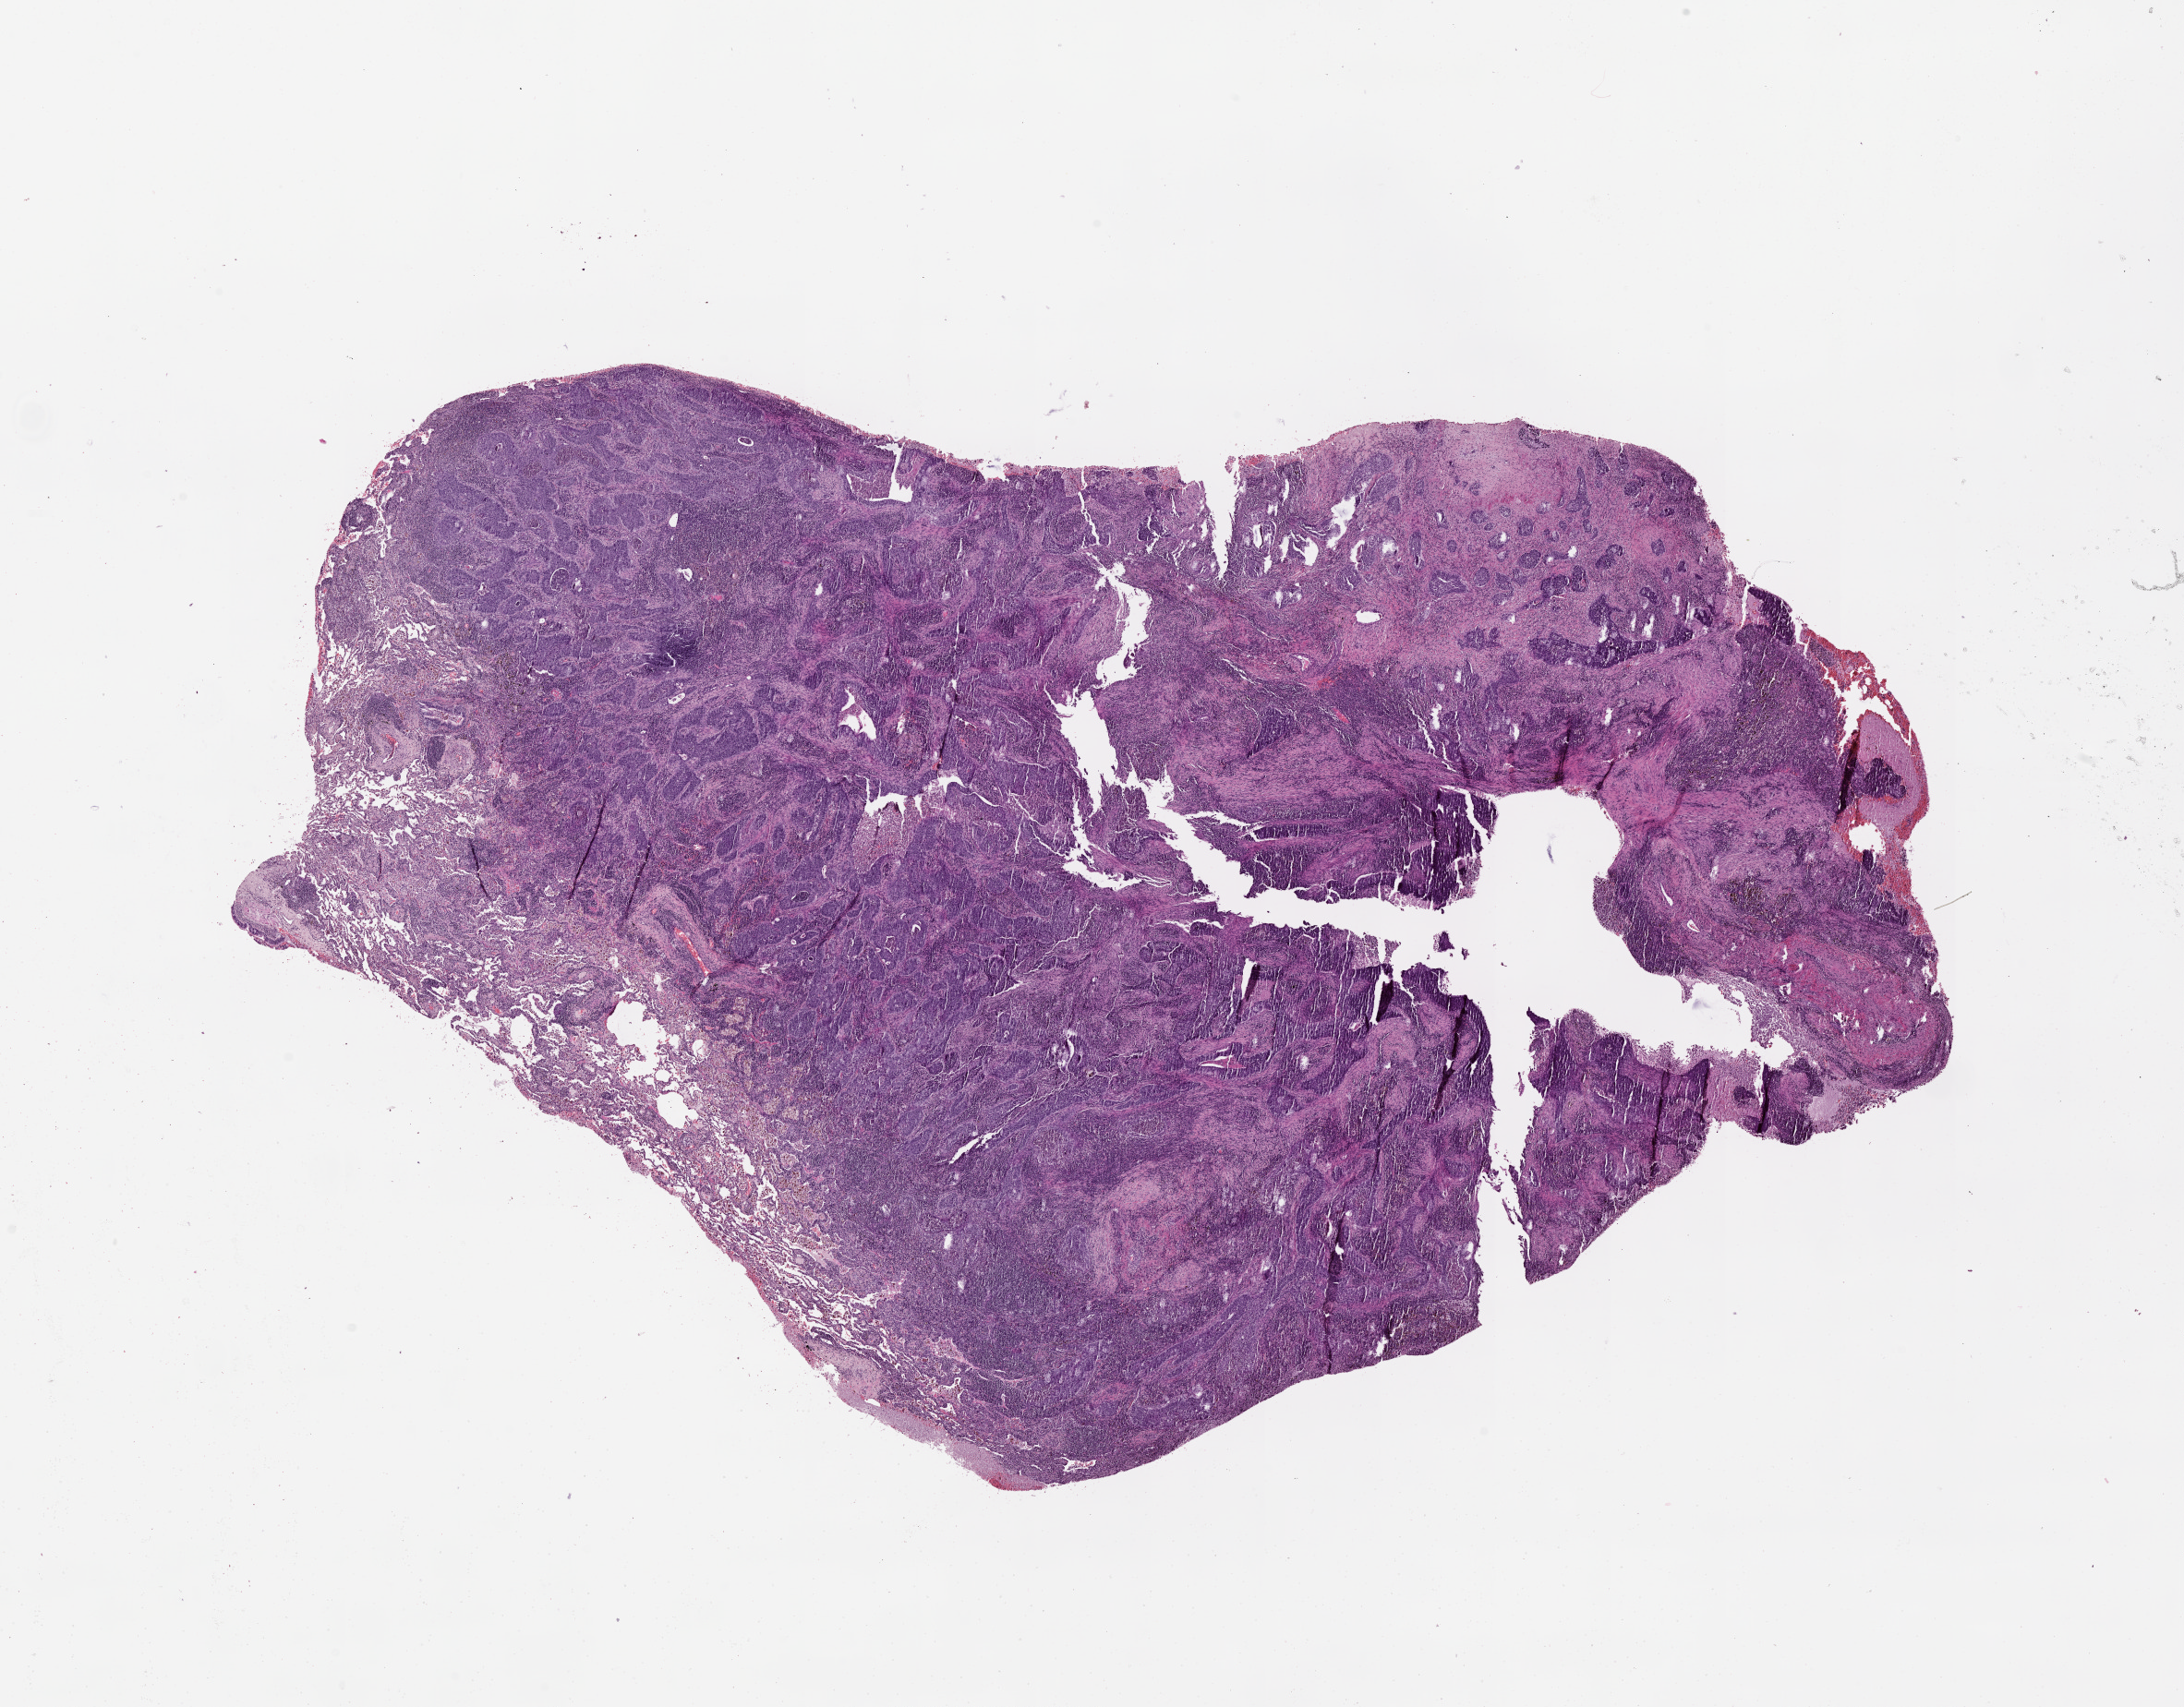
Digitized H&E-stained tissue section (whole slide) — whole scanned area (about 19.0 x 14.9 mm, acquisition: 20x scan) shown as a low-resolution overview; lung, tumour tissue. Patient: male, age 59 years.
Patient diagnosis (cohort enrolment): squamous cell carcinoma (lung).